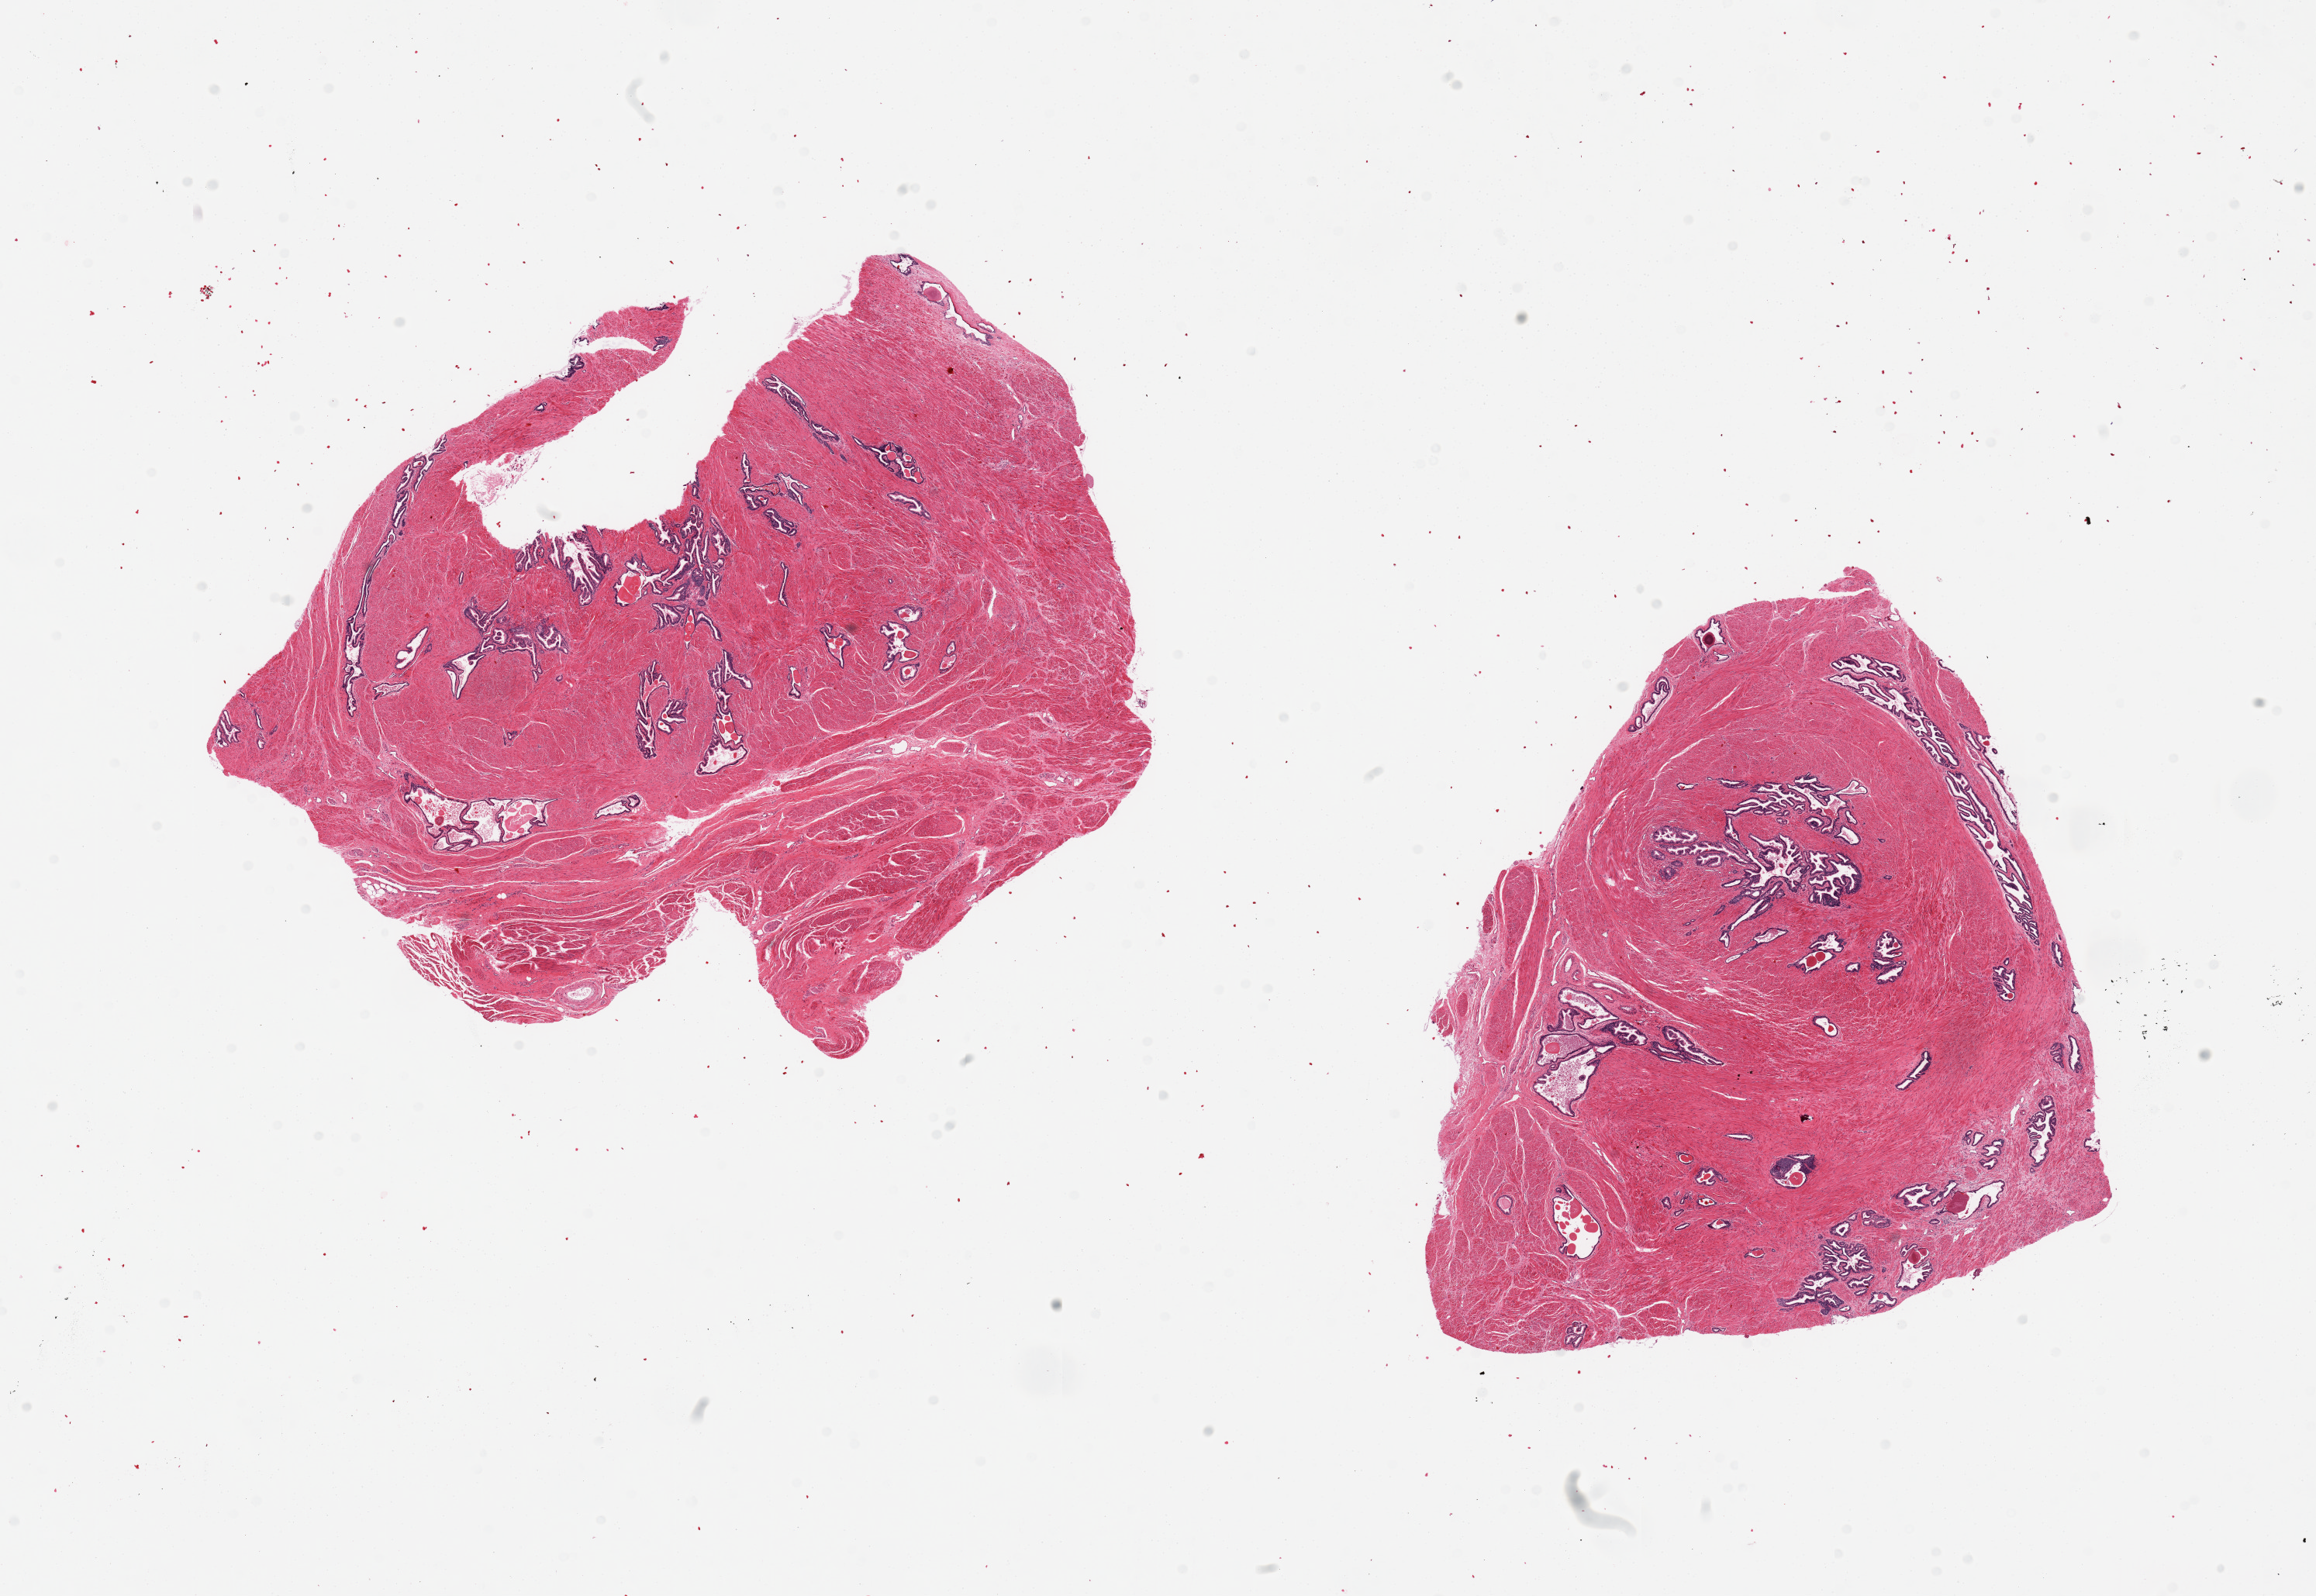
Digitized haematoxylin and eosin-stained section, a low-resolution overview of the entire scanned area, about 23.6 x 16.3 mm (from a 20x scan). PAXgene-fixed, paraffin-embedded tissue. Section of prostate (target tissue). Donor tissue sample. Male donor.
- pathologist's review note for this sample: 2 pieces